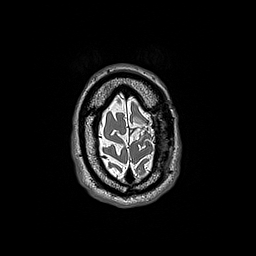
Brain MRI from a brain-tumour surgery series, one axial slice; slice 35 of 192 in the series (ordered by position); 1 mm slice thickness; 256 × 256 image matrix. From the clinical record (not read from this slice): histopathology: Oligodendroglioma; WHO grade: 3; IDH mutation: yes.
Outlined on this slice (manually delineated by an expert):
- tumour: box from (x=134, y=117) to (x=145, y=130) px